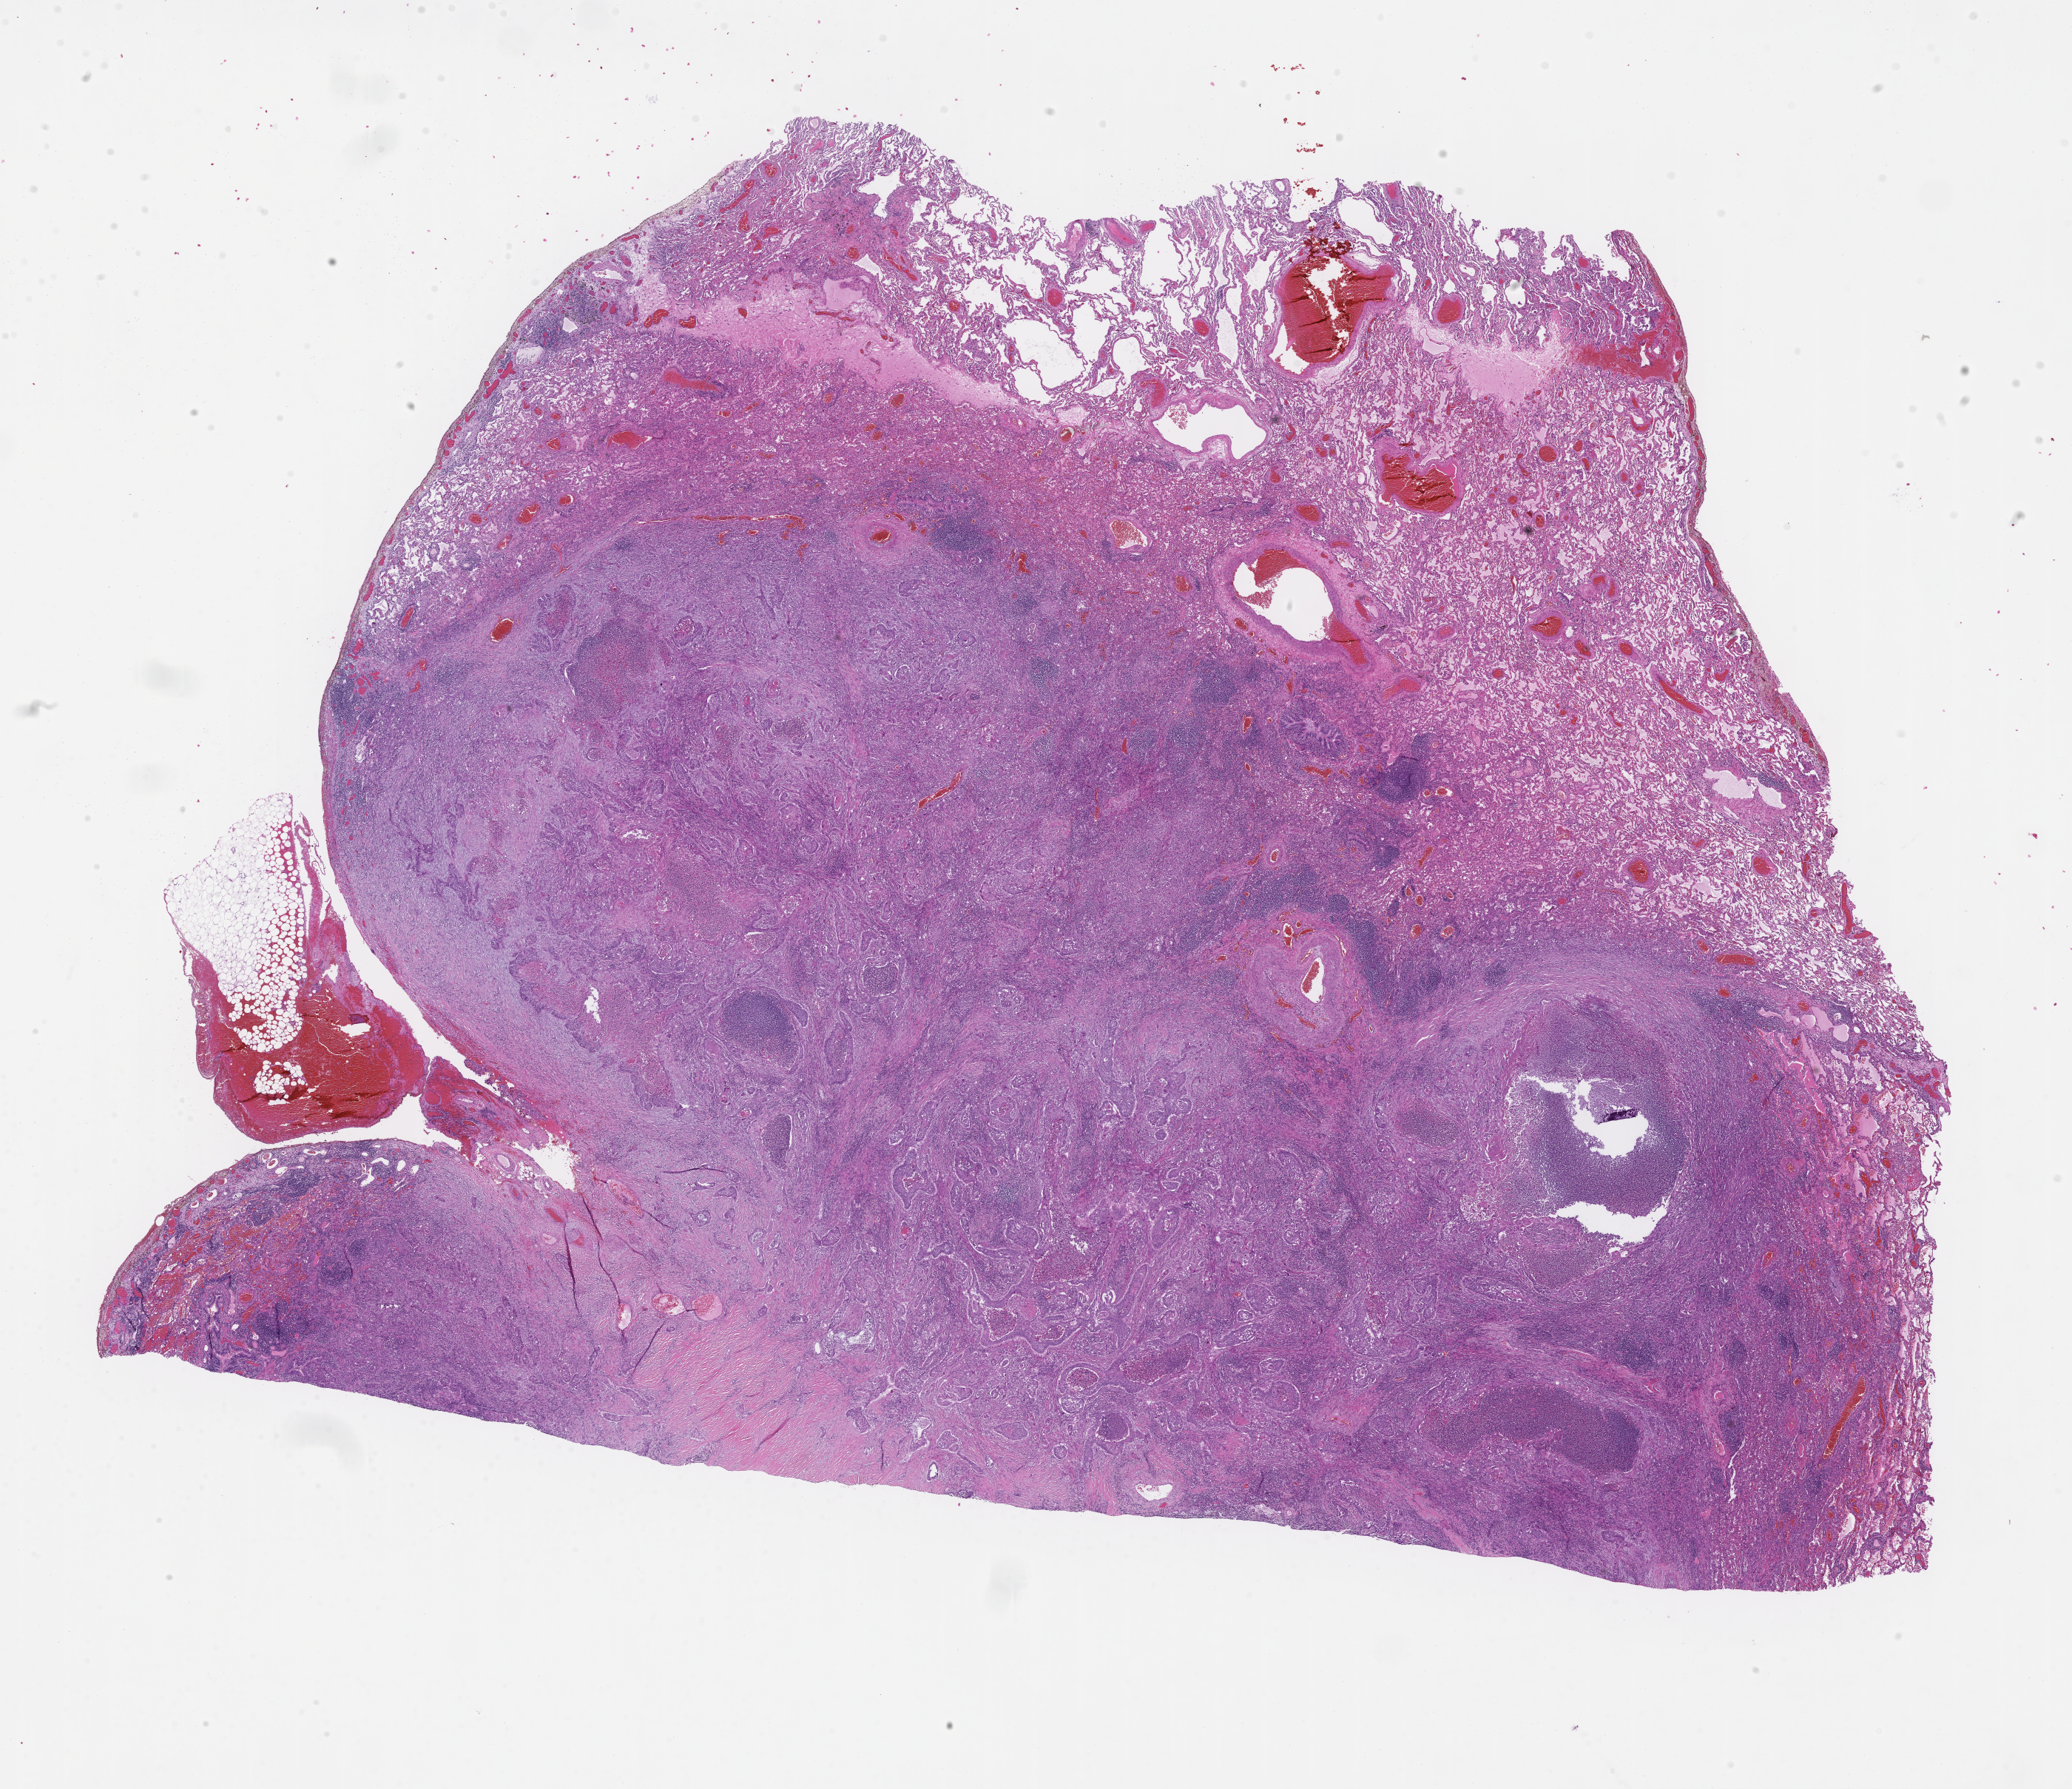
H&E whole-slide image, low-resolution overview of the scanned area, about 22.6 x 19.5 mm. Formalin-fixed paraffin-embedded section. Site: lung. Specimen time point: archival tissue. Patient sex: female.
This section: primary tumour tissue. Diagnosis: Non-Small Cell Lung Carcinoma.